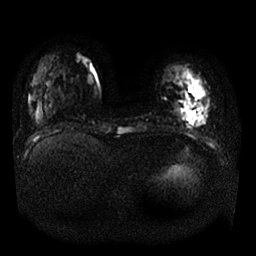
Breast MRI, one axial slice; slice 6 of 25 in the series (ordered by position); diffusion-weighted series; image 2 of 4 stored at this slice position (different b-values; order by instance number); 1.5 T; 4 mm slice thickness; 256 × 256 image matrix. Female patient.
Outlined on this slice (manually delineated by an expert):
- tumour on diffusion-weighted imaging: bounding box [x1, y1, x2, y2] px = [184, 96, 196, 117]